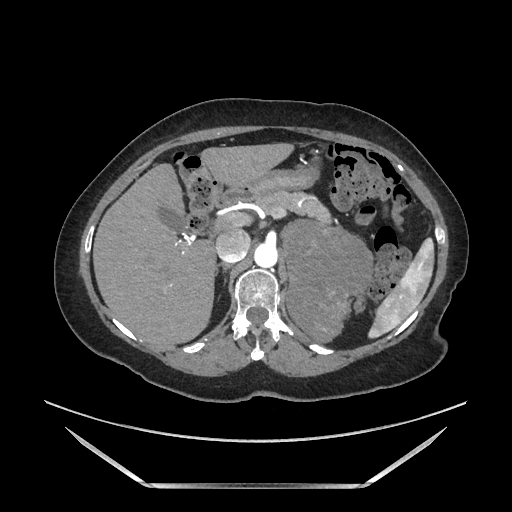
Contrast-enhanced abdominal CT, one axial slice; position 115 of 205 along the scan axis; soft-tissue window (W 400 / L 40 HU); 1.25 mm slice thickness; 512 × 512 image matrix, field of view 440 × 440 mm. Female patient. From the clinical record (not read from this slice): diagnosis: adrenocortical carcinoma; tumour side: left adrenal.
Outlined on this slice (semi-automatically segmented with operator editing):
- mass: bounding box <288,223,368,337> (left, top, right, bottom; pixels)